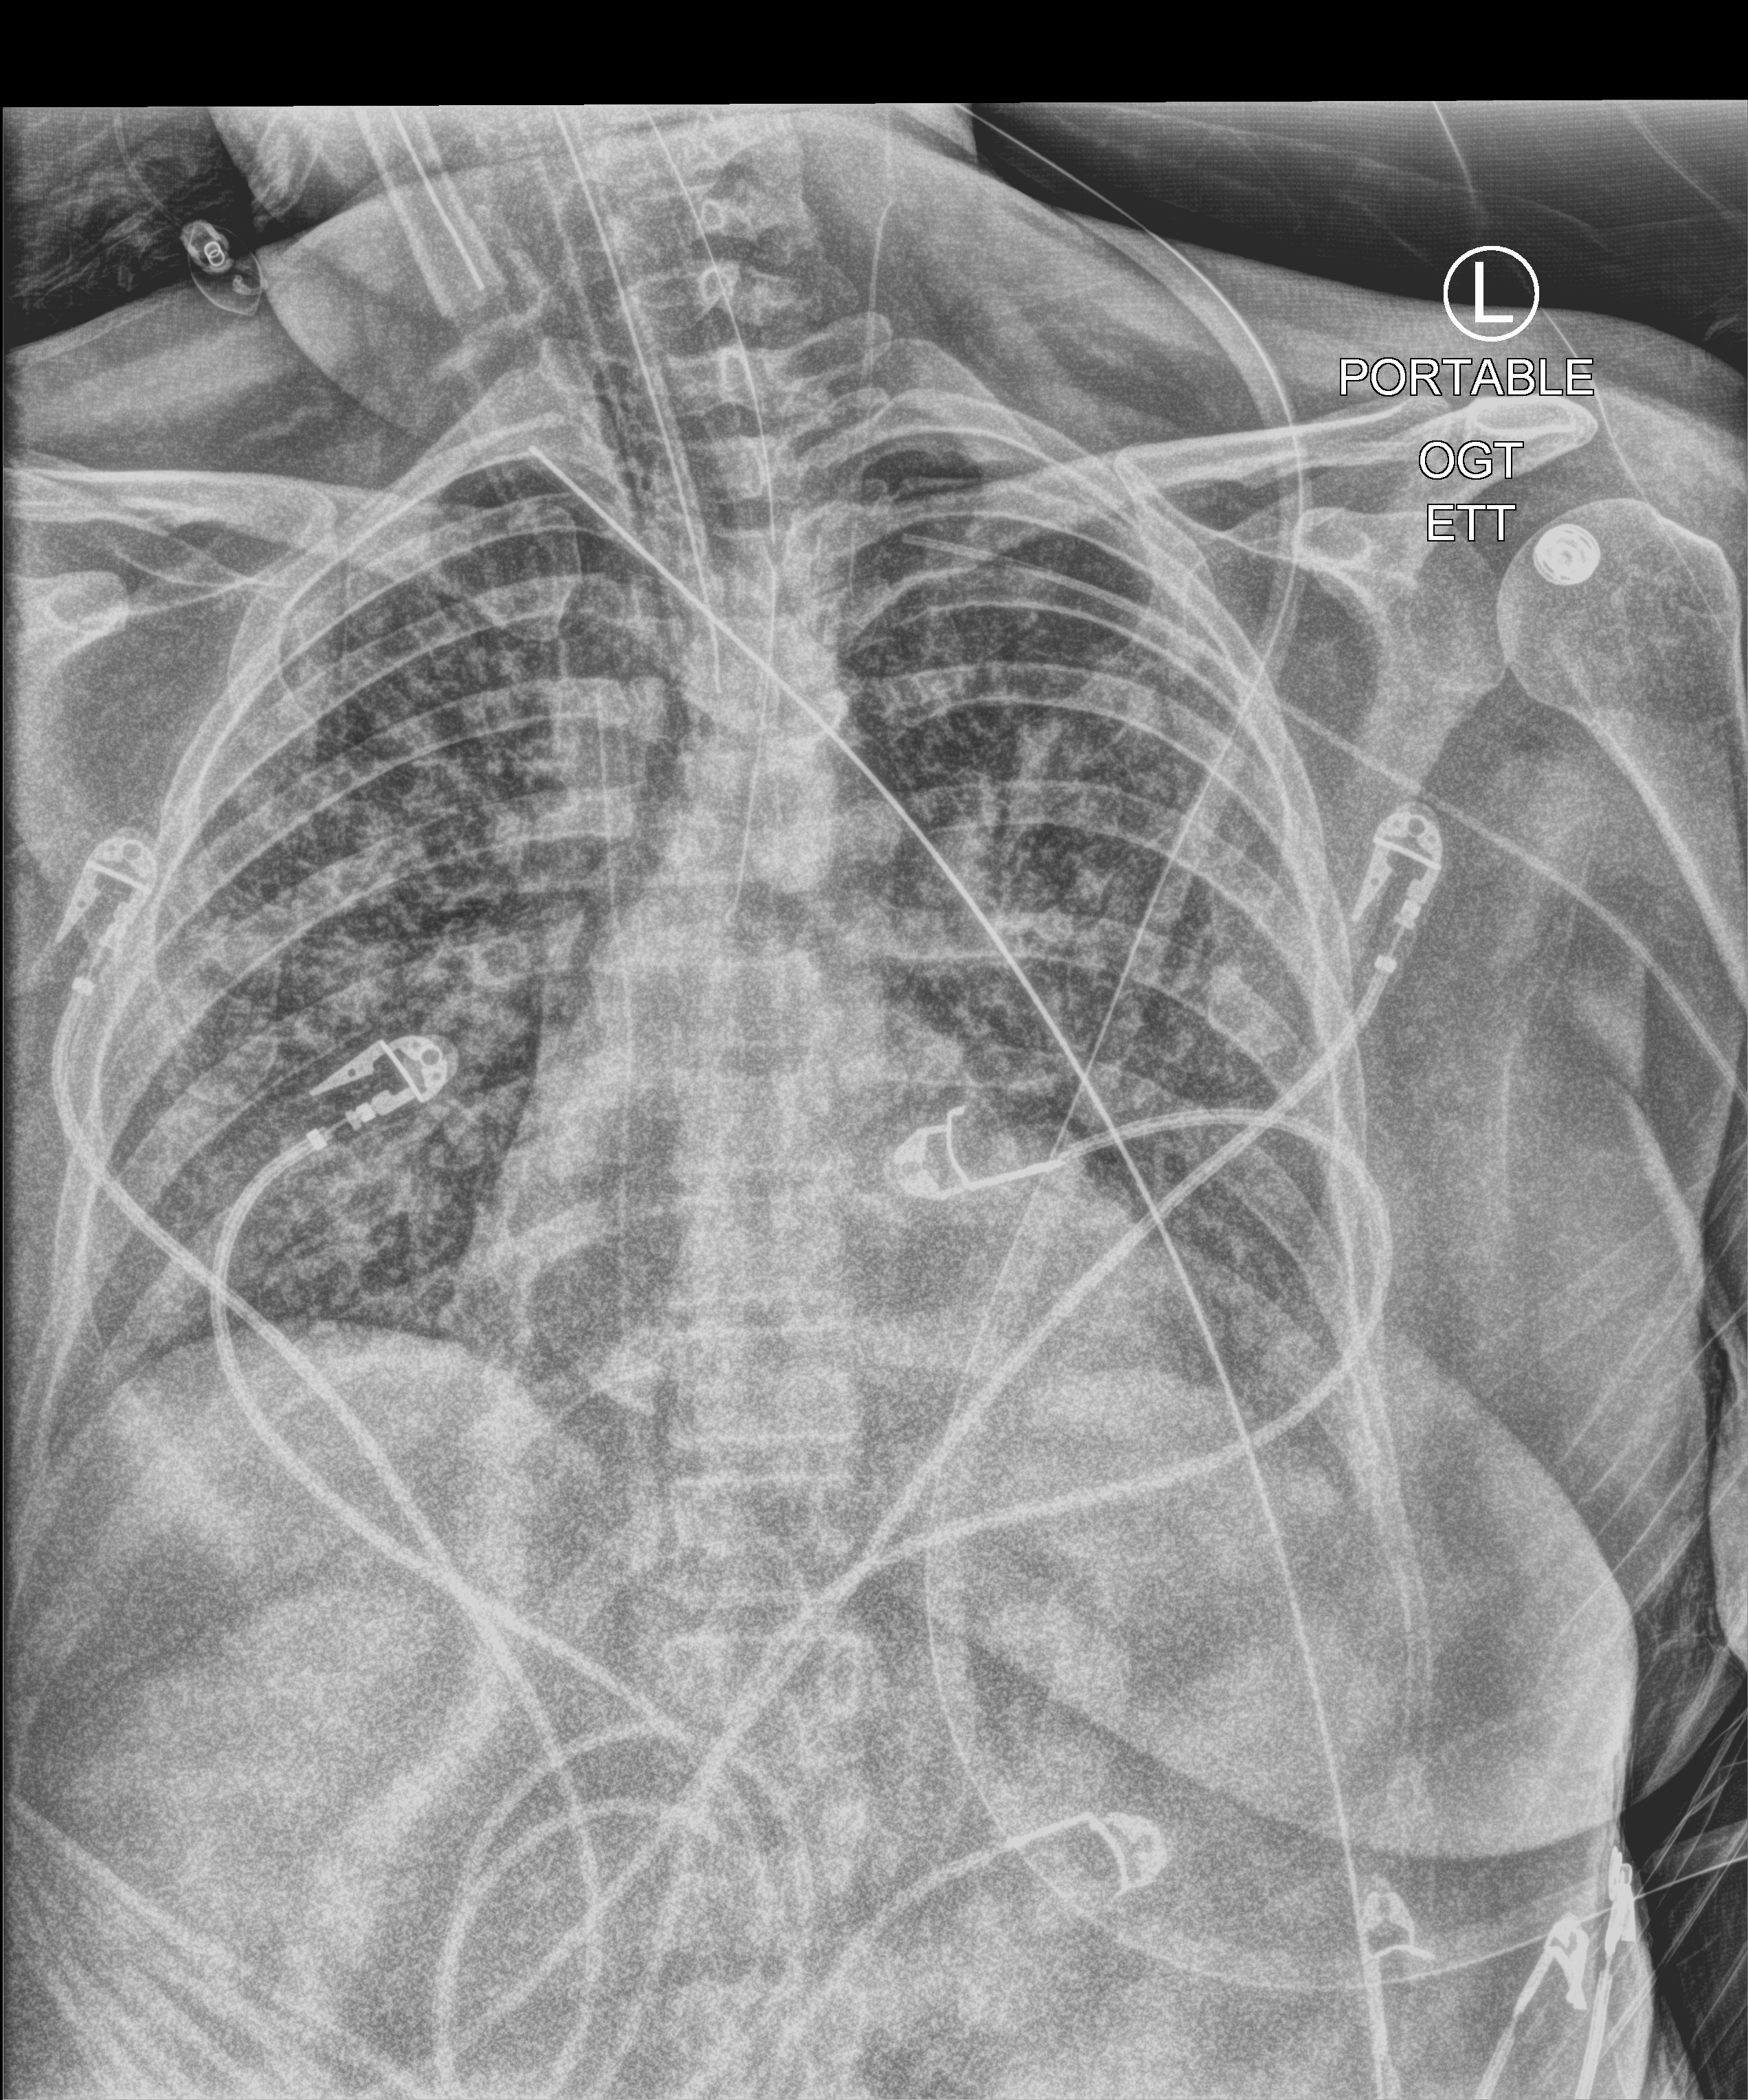
Portable chest radiograph, anteroposterior (AP) projection. Patient hospitalised with COVID-19; female, aged 18–59 years.
Admission-level facts for this patient (not findings on this image; timing relative to this image not recorded): mechanically ventilated during this hospital stay: yes.